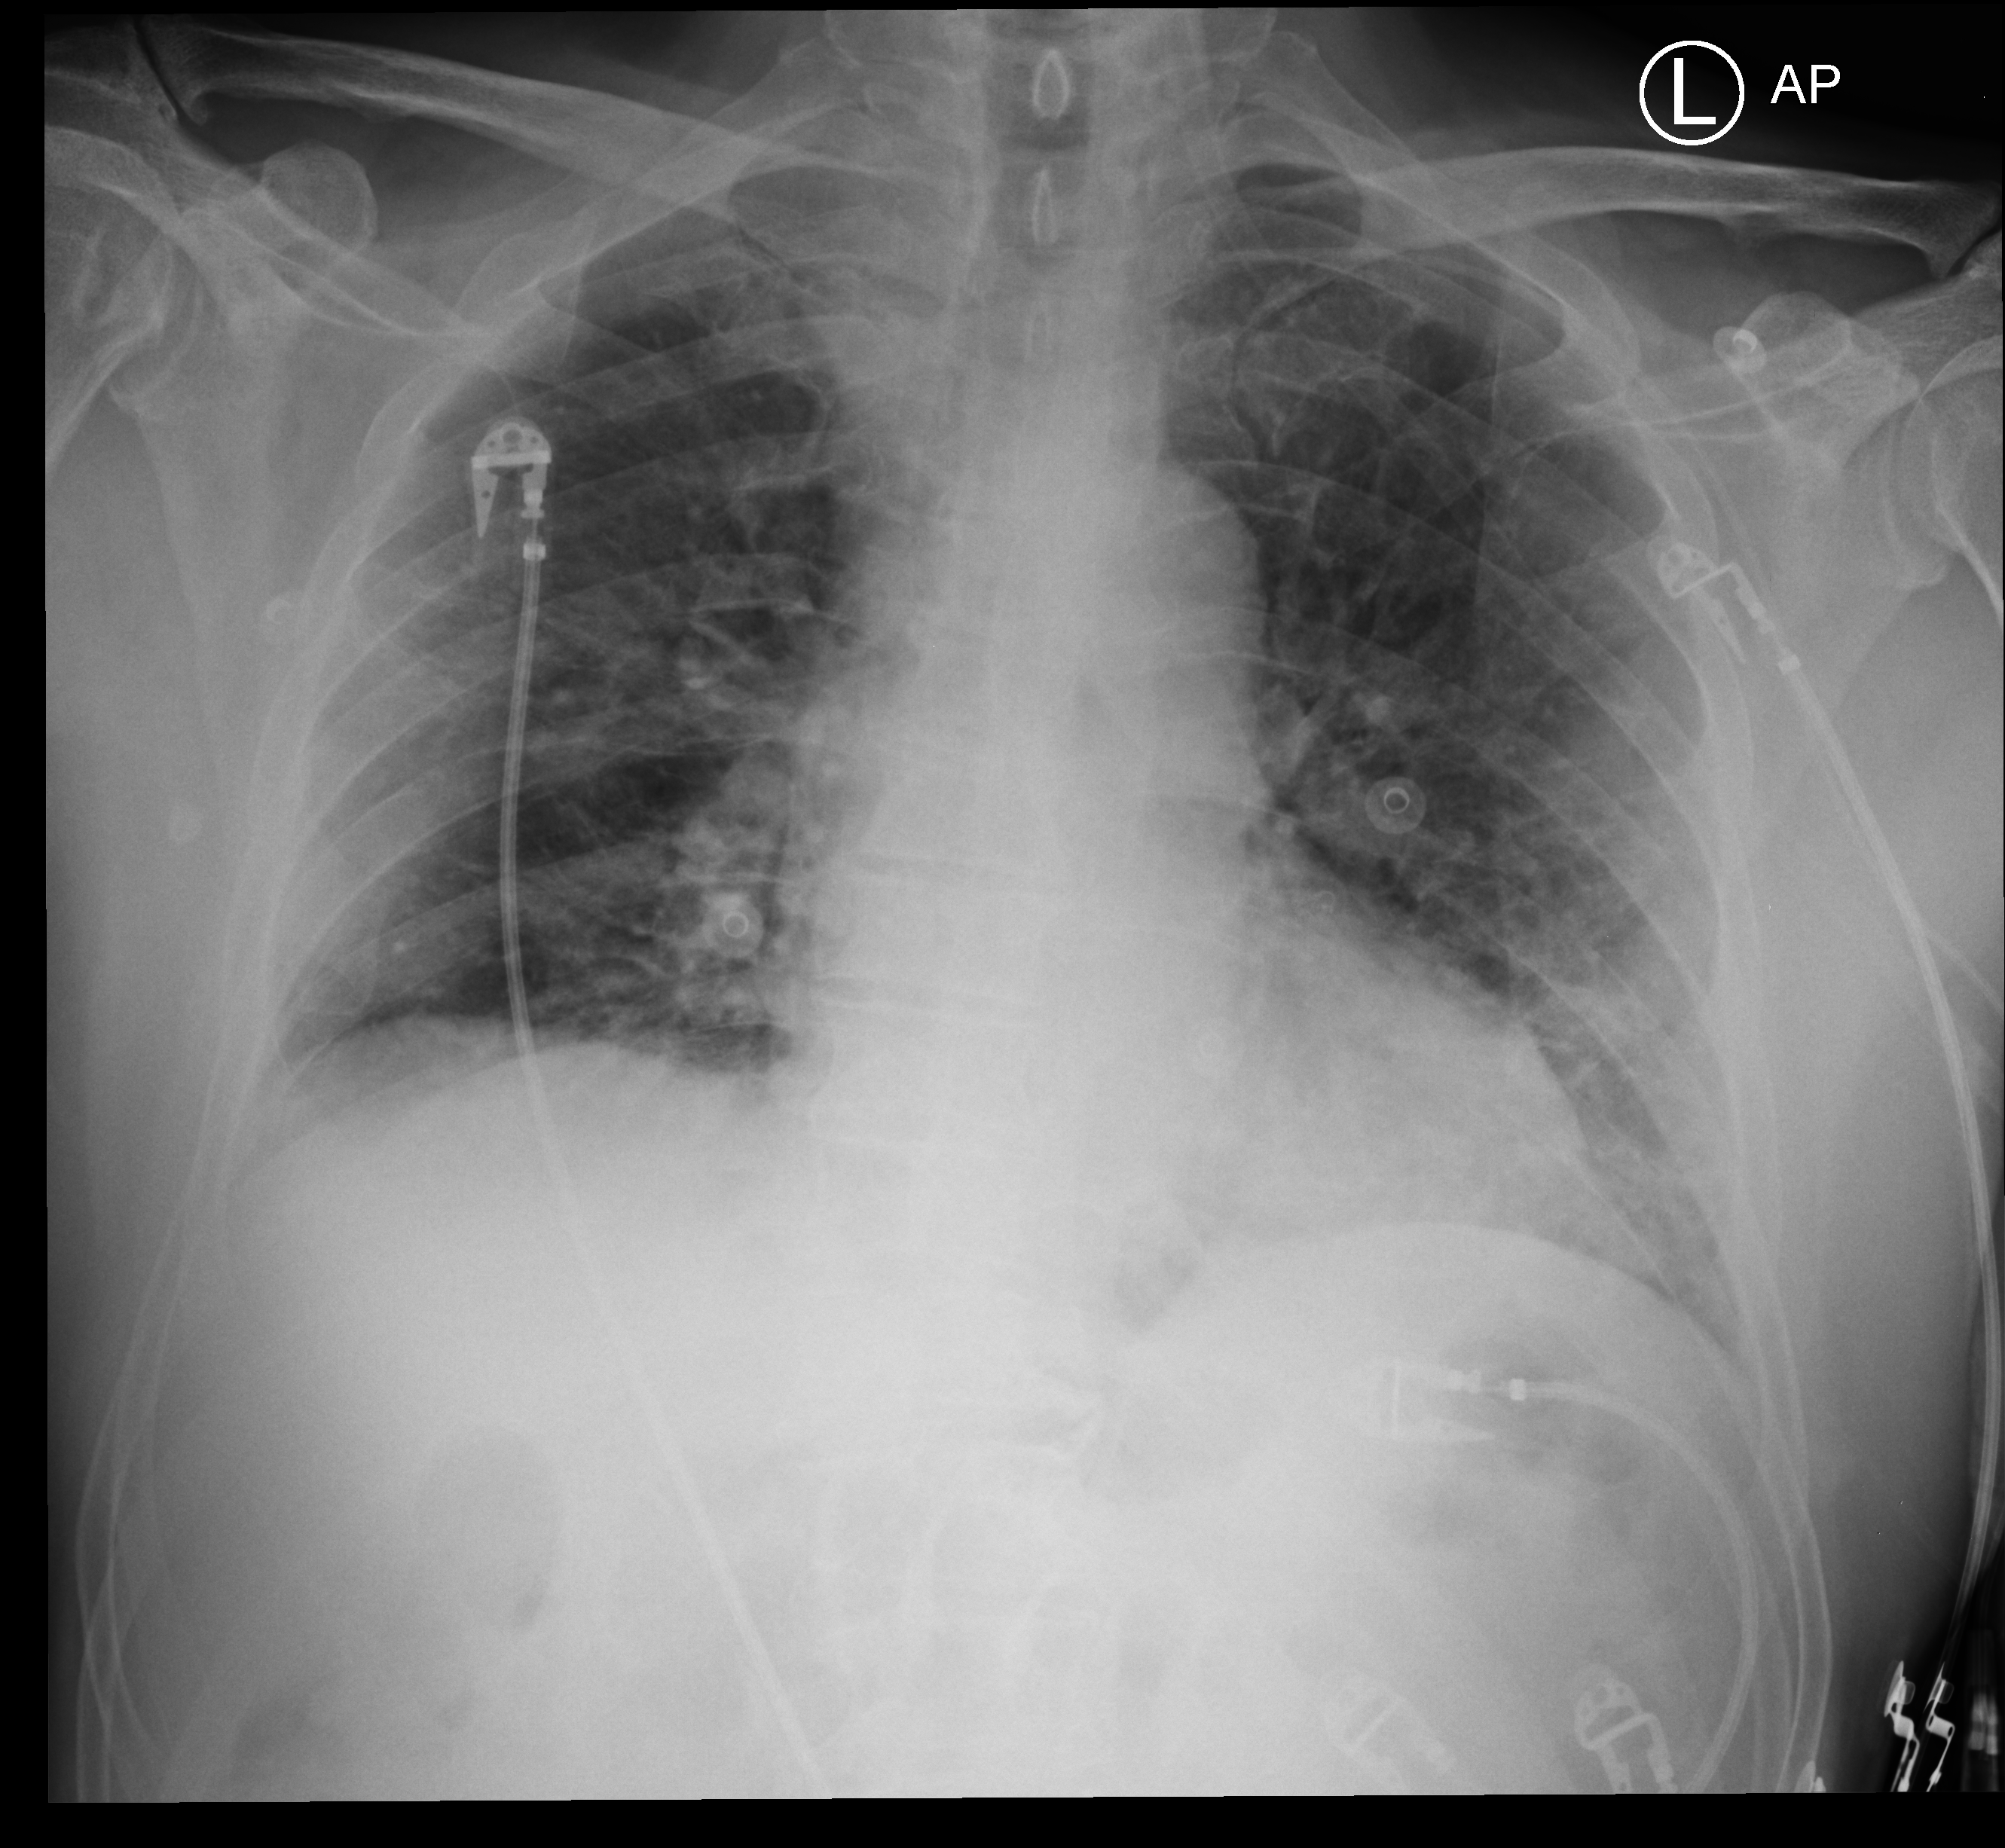
Bedside chest radiograph (computed radiography), anteroposterior (AP) projection. Patient hospitalised with COVID-19; male, aged 60–74 years.
Admission-level facts for this patient (not findings on this image; timing relative to this image not recorded): COPD (admission record): no; length of hospital stay: 14 days.